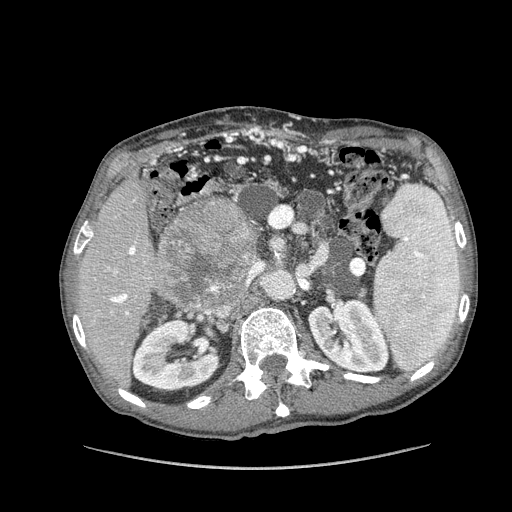
Contrast-enhanced abdominal CT (liver protocol), one axial slice. Reconstruction kernel STANDARD. 100 kVp. Soft-tissue window (W 400 / L 40 HU). 512 × 512 image matrix, field of view 400 × 400 mm. From the clinical record (not read from this slice): diagnosis: hepatocellular carcinoma (patient treated with transarterial chemoembolisation; whether this scan precedes or follows treatment is not stated here); TNM stage (as recorded): Stage-IIIA; Child-Pugh class: A; tumour nodularity: multinodular; tumour size: 9.9 cm.
Annotated regions visible in this slice (semi-automatically segmented with operator editing):
- liver parenchyma outside the tumour (the mass and vessels are separate outlines, so this box may not span the whole liver): bounding box (x1, y1, x2, y2) in pixels: (78, 172, 182, 382)
- mass: (157, 199, 259, 309)
- liver vessels: (90, 200, 145, 315)